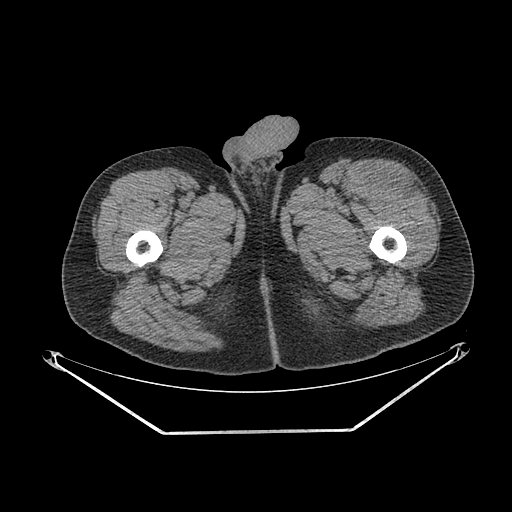
CT of an extremity soft-tissue mass (from a PET/CT study), one axial slice; slice 259 of 267 in the series (ordered by position); soft-tissue window (W 400 / L 40 HU); 512 × 512 image matrix, field of view 500 × 500 mm. Male patient. From the clinical record (not read from this slice): histological type: extraskeletal osteosarcoma; grade: high; site of the primary tumour: thigh.
Outlined on this slice (expert contour drawn on MRI and transferred to this co-registered scan by the dataset authors):
- gross tumour volume (mass): bounding box <377,171,417,193> (left, top, right, bottom; pixels)